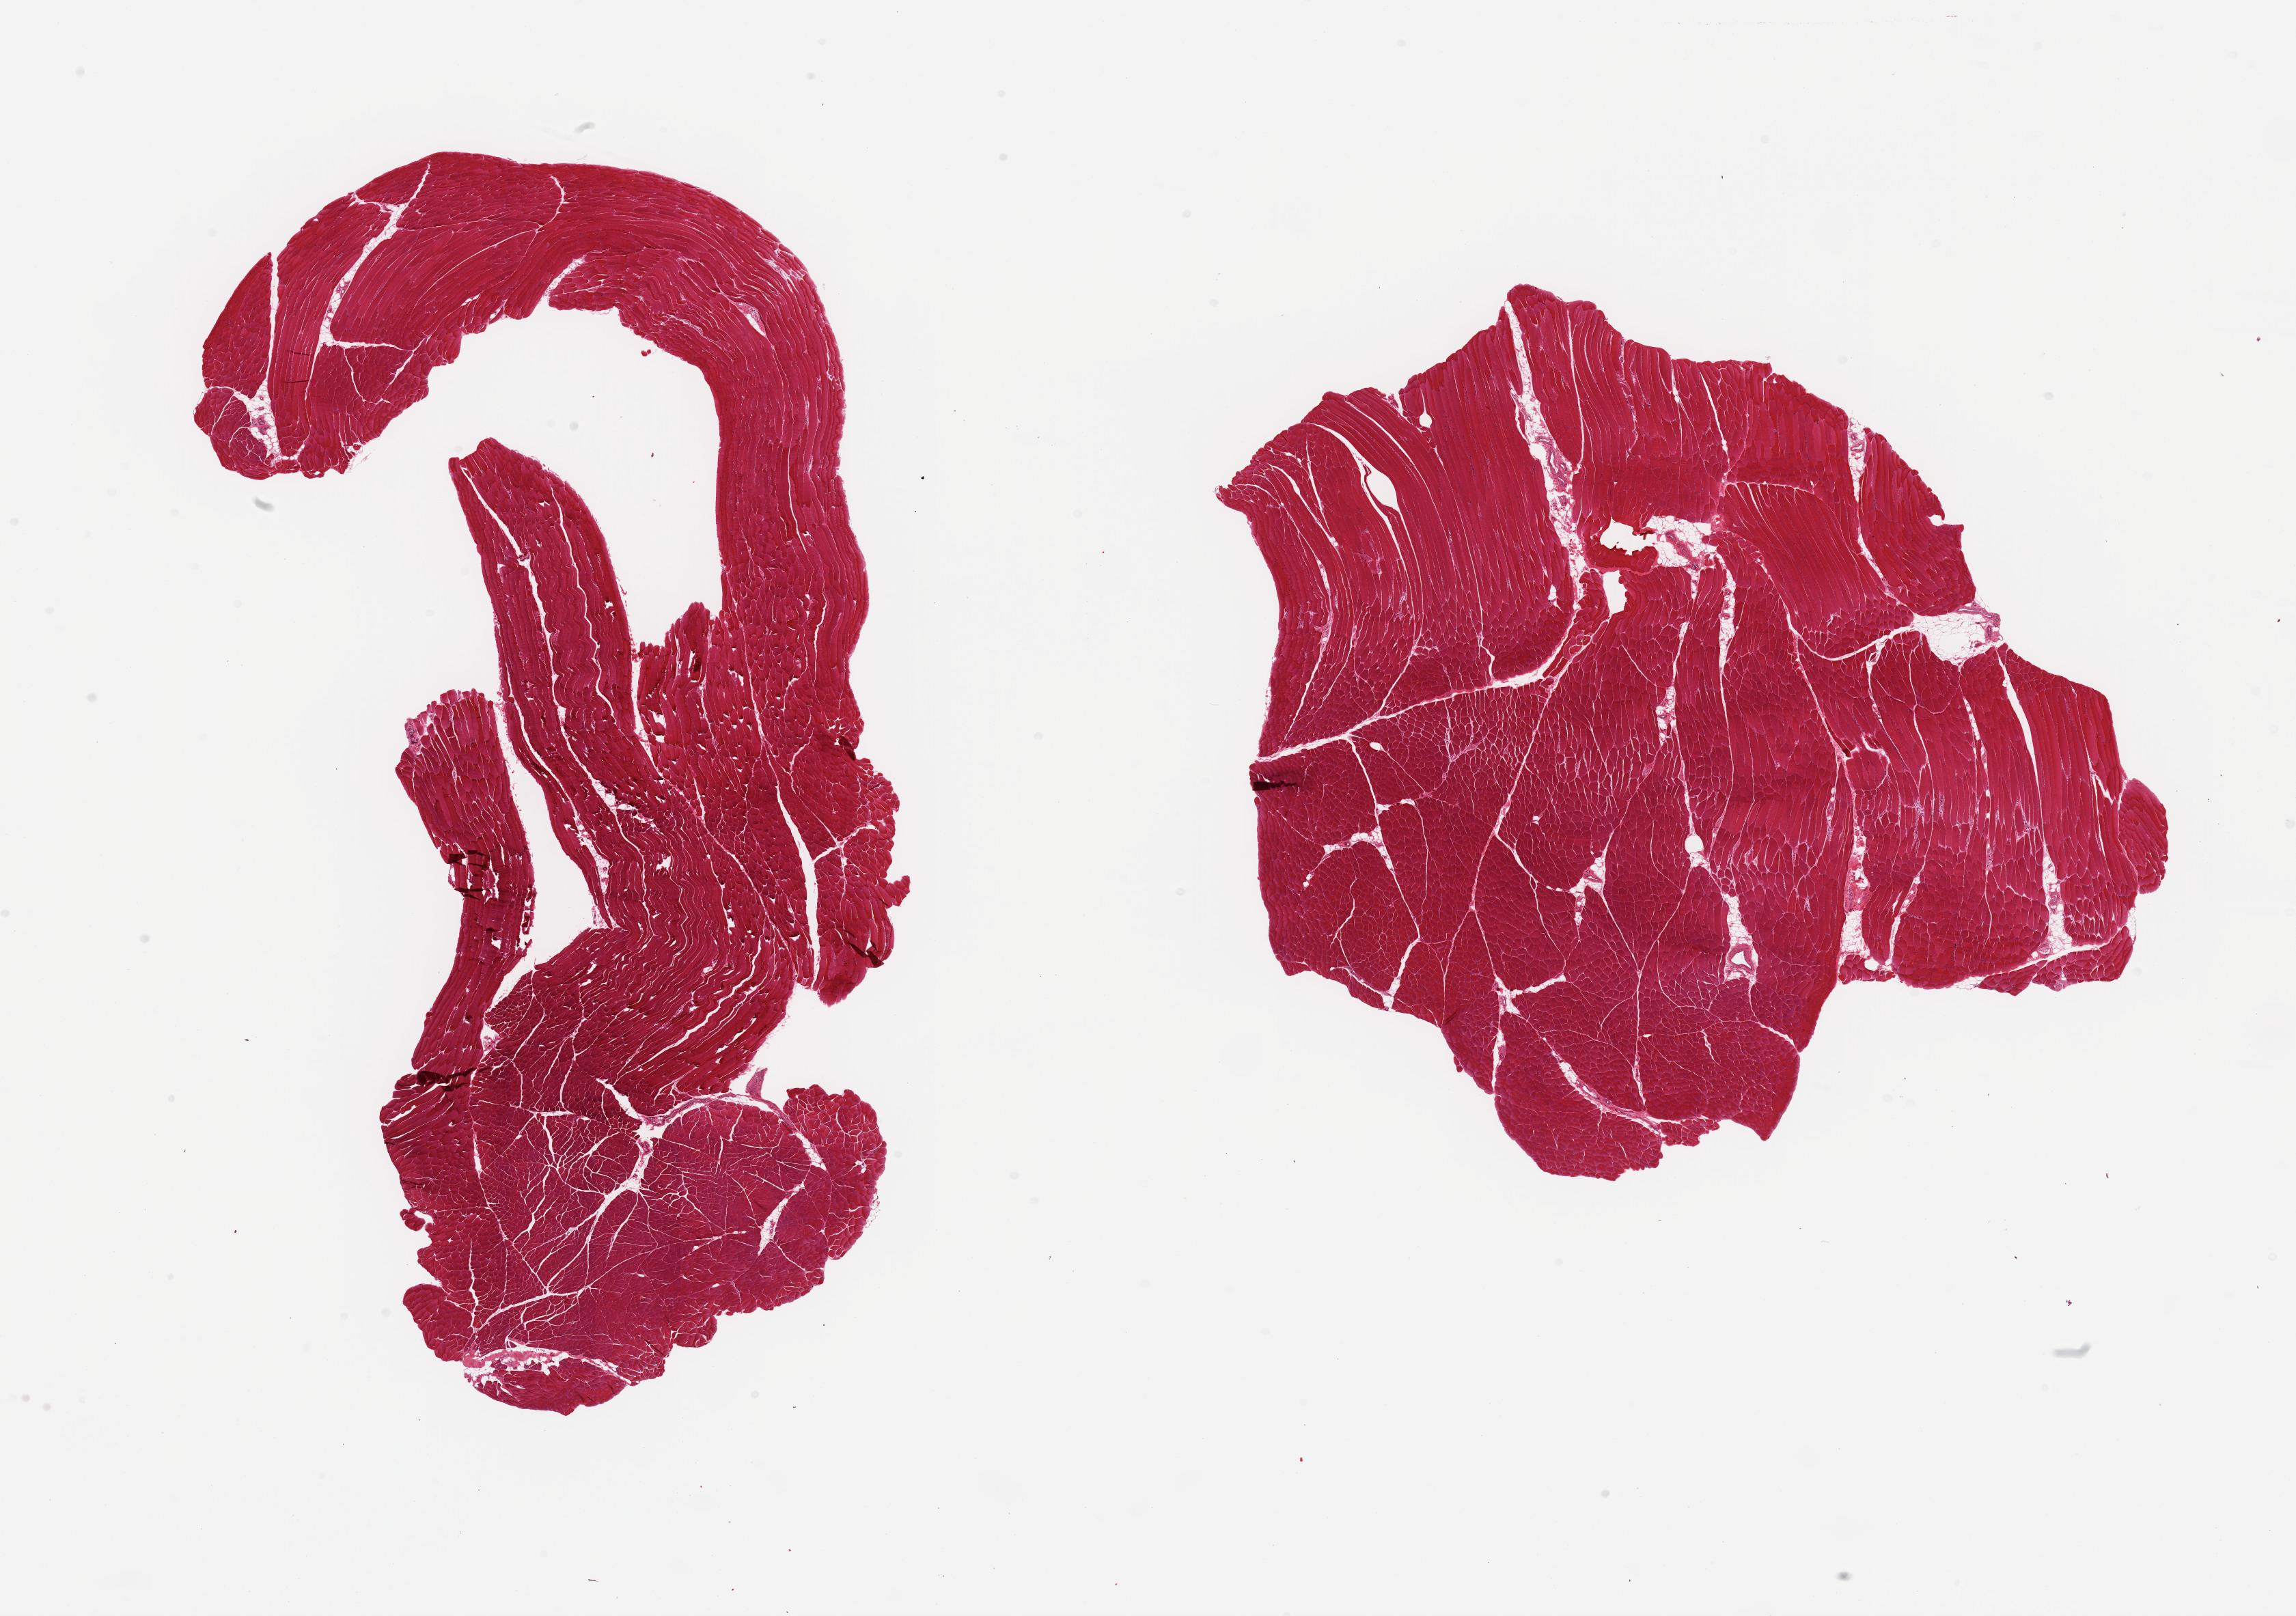
Haematoxylin and eosin whole-slide image — a low-resolution overview of the entire scanned area, about 26.6 x 18.7 mm, PAXgene-fixed paraffin-embedded (PFPE) section, target tissue: skeletal muscle, donor tissue sample. Donor: male.
Review note (as recorded): 2 pieces, trace-minimal interstitial fat,~10%.